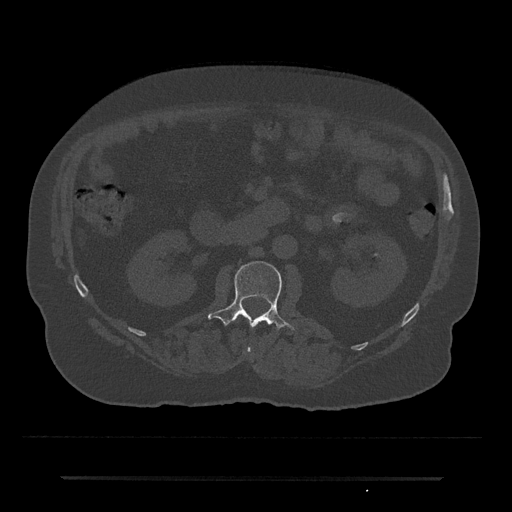
CT including the spine, one axial slice; slice 19 of 797 in the series (ordered by position); reconstruction kernel Br40s/3; 120 kVp; bone window (W 1800 / L 400 HU); 0.5 mm slice thickness; 512 × 512 image matrix. Patient: male, 69 years. Case-level facts recorded for this patient, not image findings: primary cancer: prostate.
Structures marked on this image (semi-automatically segmented with operator editing):
- L1 vertebra: bounding box (x1, y1, x2, y2) in pixels: (247, 346, 251, 353)
- L2 vertebra: (208, 261, 295, 331)